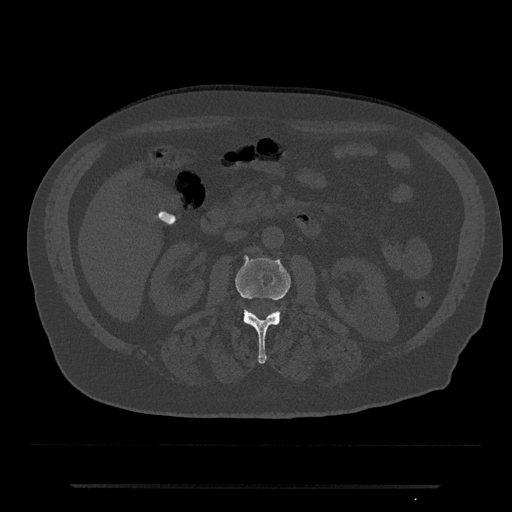
CT including the spine, one axial slice; position 462 of 797 along the scan axis; 120 kVp; bone window (W 1800 / L 400 HU); 0.5 mm slice thickness; 512 × 512 image matrix, field of view 434 × 434 mm. Patient: male, 80 years. From the clinical record (not read from this slice): primary cancer: prostate; vertebrae with lytic lesions (as recorded): L1, T11.
Outlined on this slice (semi-automatic segmentation, software-assisted and operator-edited):
- L2 vertebra: box from (x=235, y=255) to (x=291, y=363) px